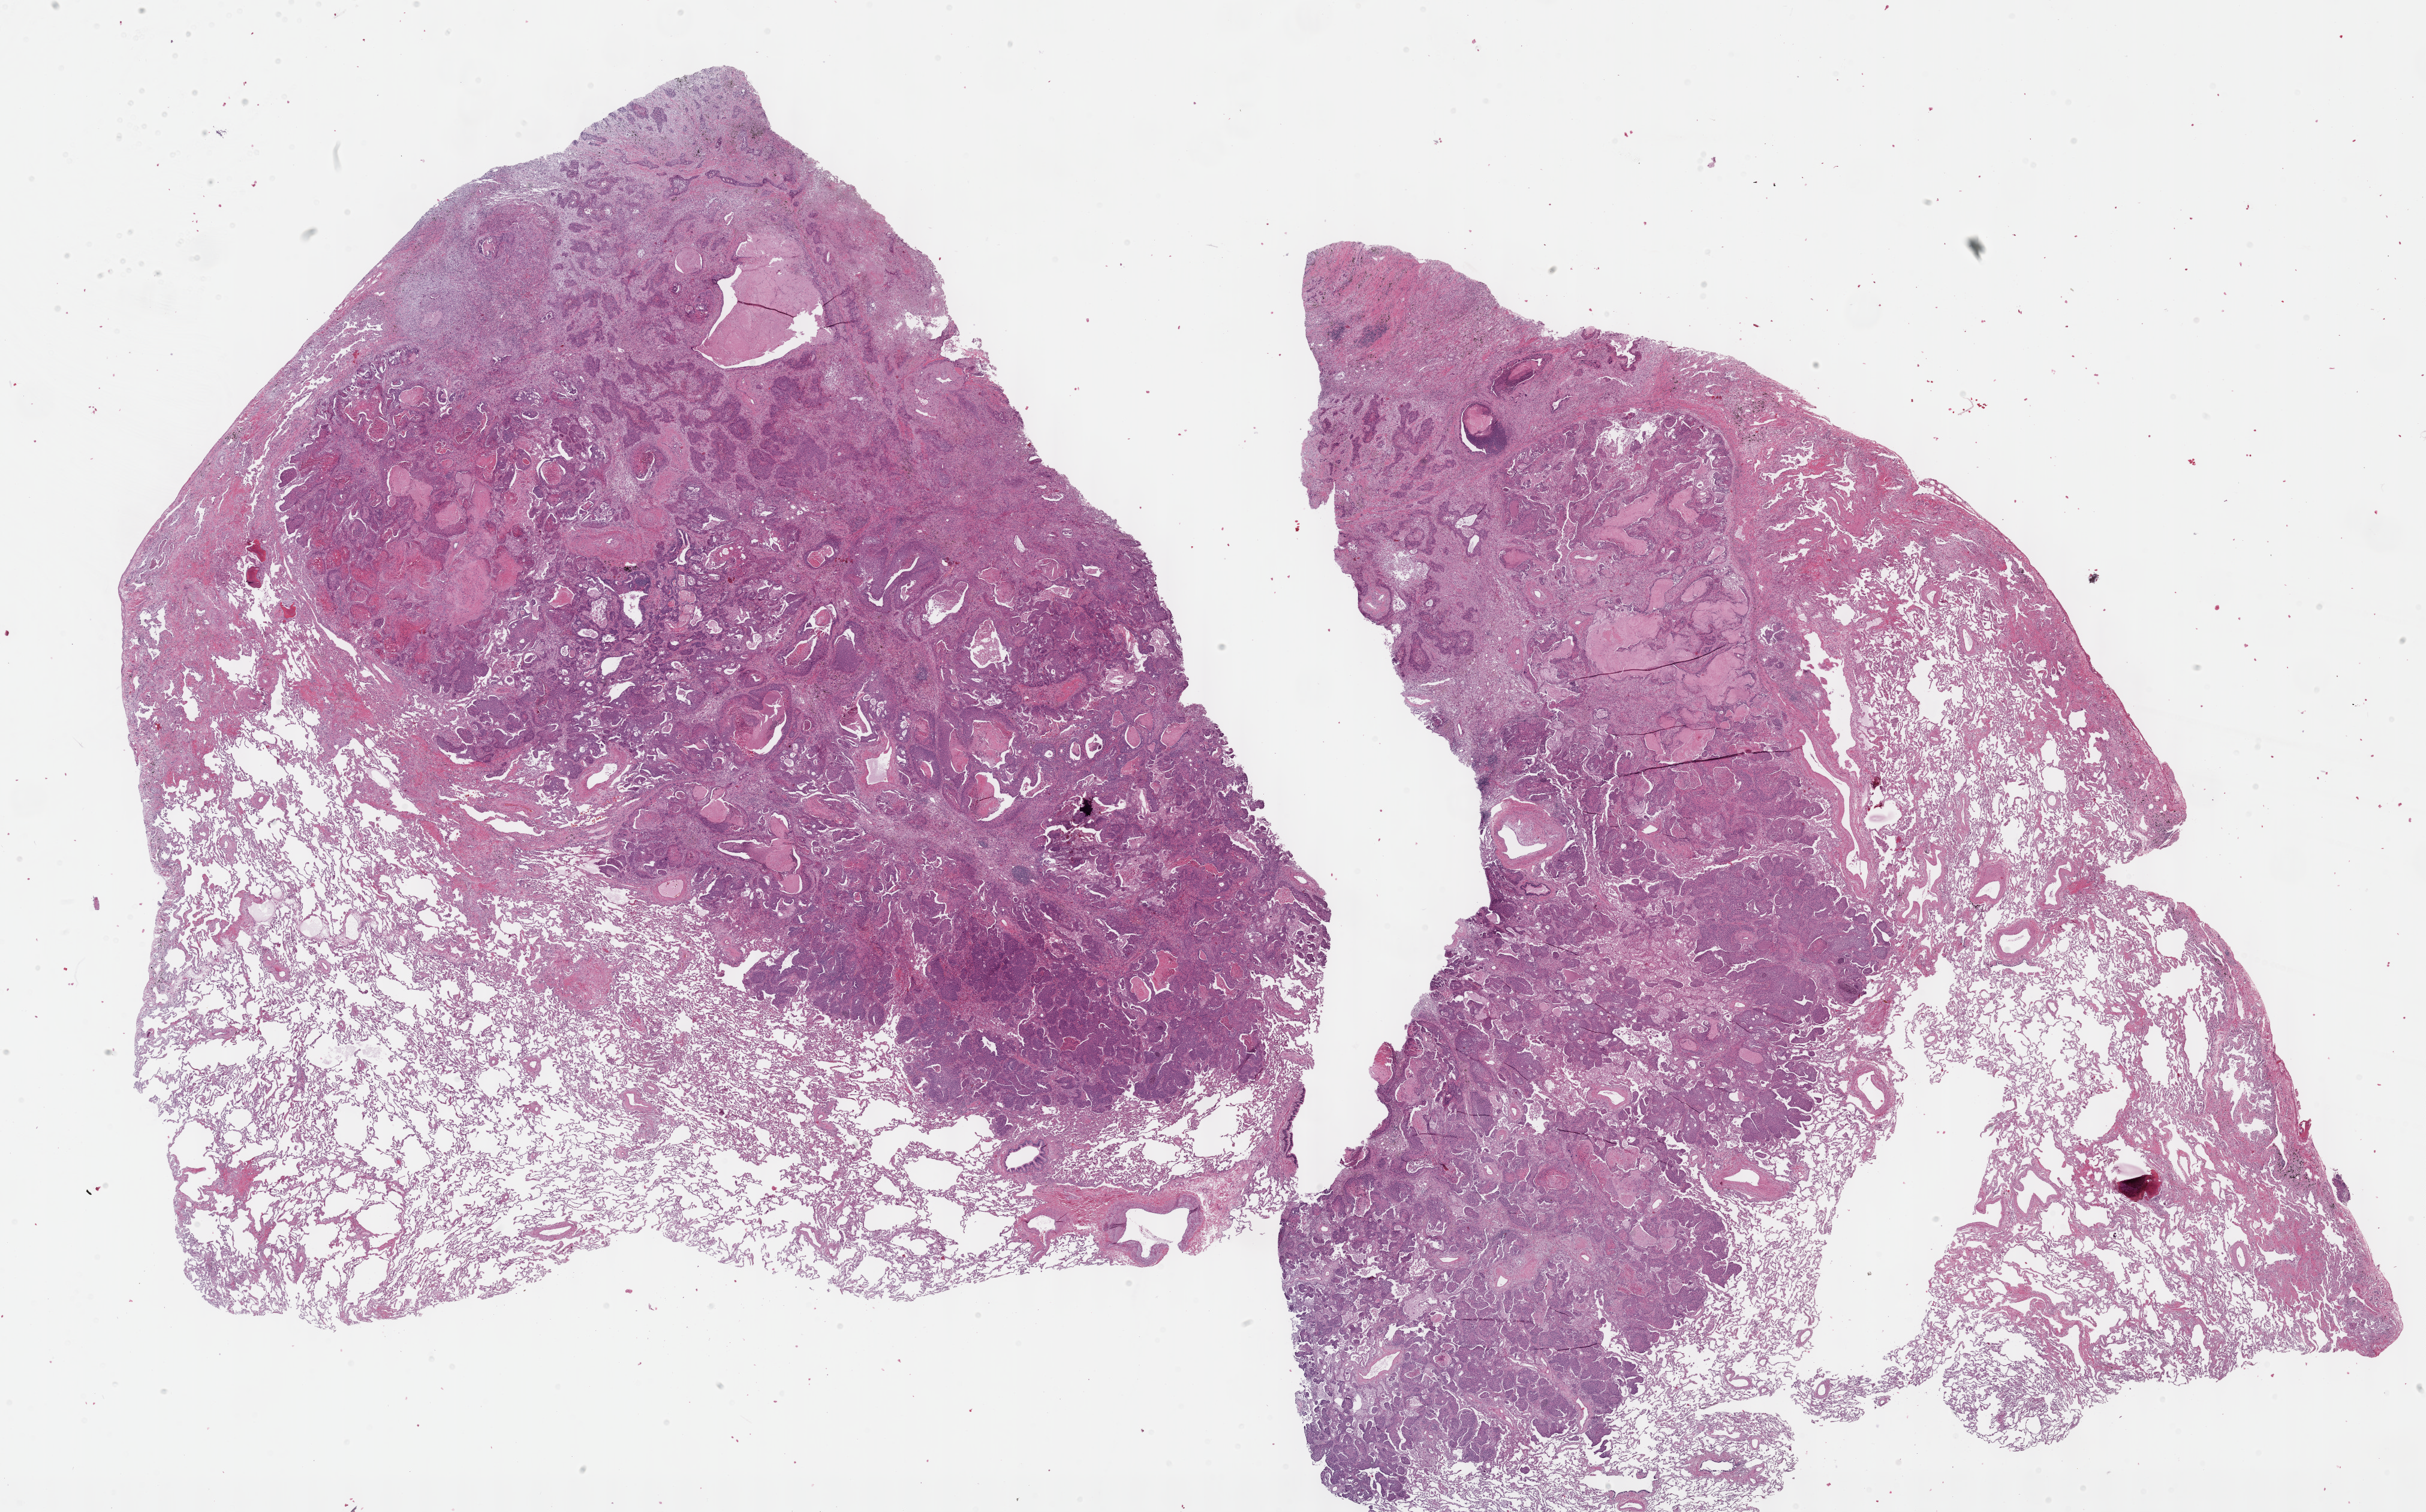
Hematoxylin and eosin (H&E) stained whole-slide image — low-resolution overview of the scanned area, about 32.7 x 20.4 mm (from a 40x scan). FFPE section. Sample: primary tumour, lung. Male patient; age at initial diagnosis 67 years.
Pathologic diagnosis: Squamous cell carcinoma, NOS (lower lobe, lung).